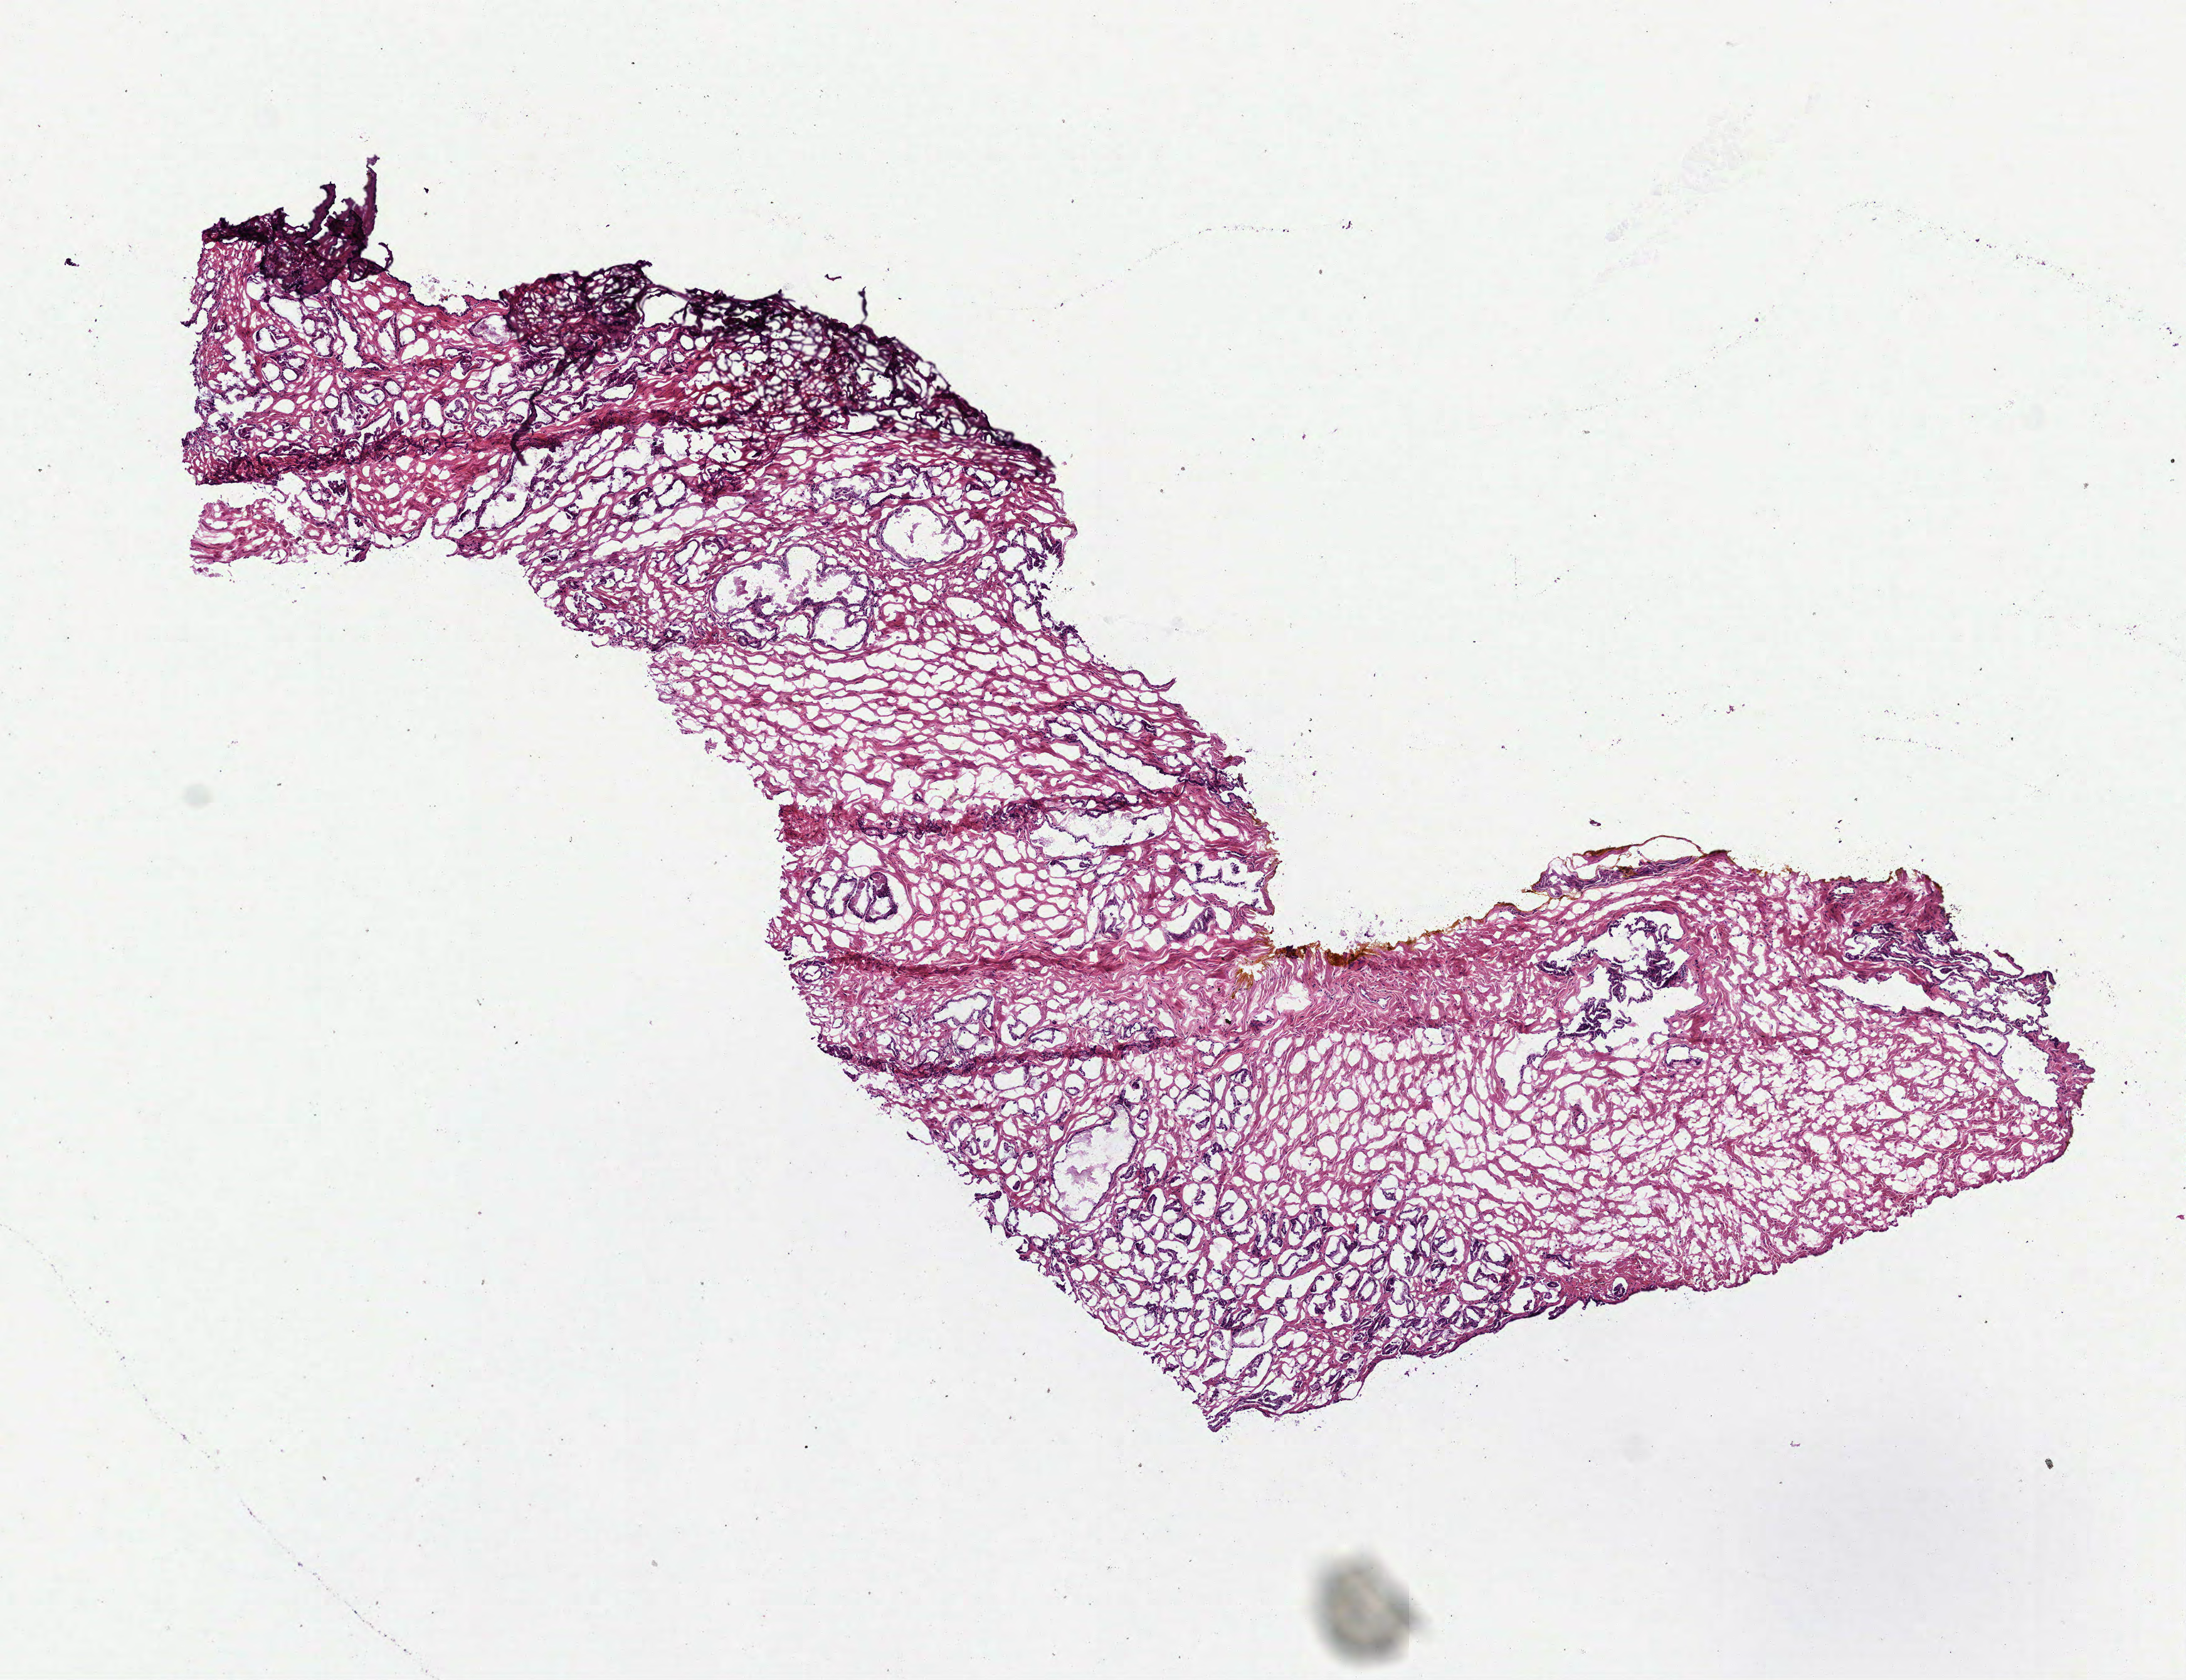
H&E-stained whole-slide image — low-resolution overview of the scanned area, about 7.0 x 5.4 mm (from a 40x scan), frozen section from the bottom of the tissue portion, primary tumour sample from the prostate. Male, age 58 years at initial diagnosis. Gleason score: 6 (3+3). Composition of this section per pathologist review: tumour cells 35%, tumour nuclei 35%, normal cells 30%, stromal cells 35%, necrosis 0%. Infiltration values recorded for this section: lymphocyte infiltration 2%, monocyte infiltration 0%, neutrophil infiltration 0%.
Laterality: bilateral. Pathologic diagnosis: Acinar cell carcinoma (prostate gland).